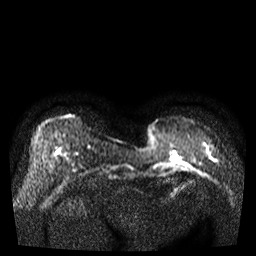
Breast MRI, one axial slice; slice 7 of 35 in the series (ordered by position); diffusion-weighted series; image 2 of 4 stored at this slice position (different b-values; order by instance number); 3 T; 5 mm slice thickness; 256 × 256 image matrix. Female patient.
Annotated regions visible in this slice (expert manual segmentation):
- tumour on diffusion-weighted imaging: bounding box (x1, y1, x2, y2) in pixels: (174, 155, 177, 161)